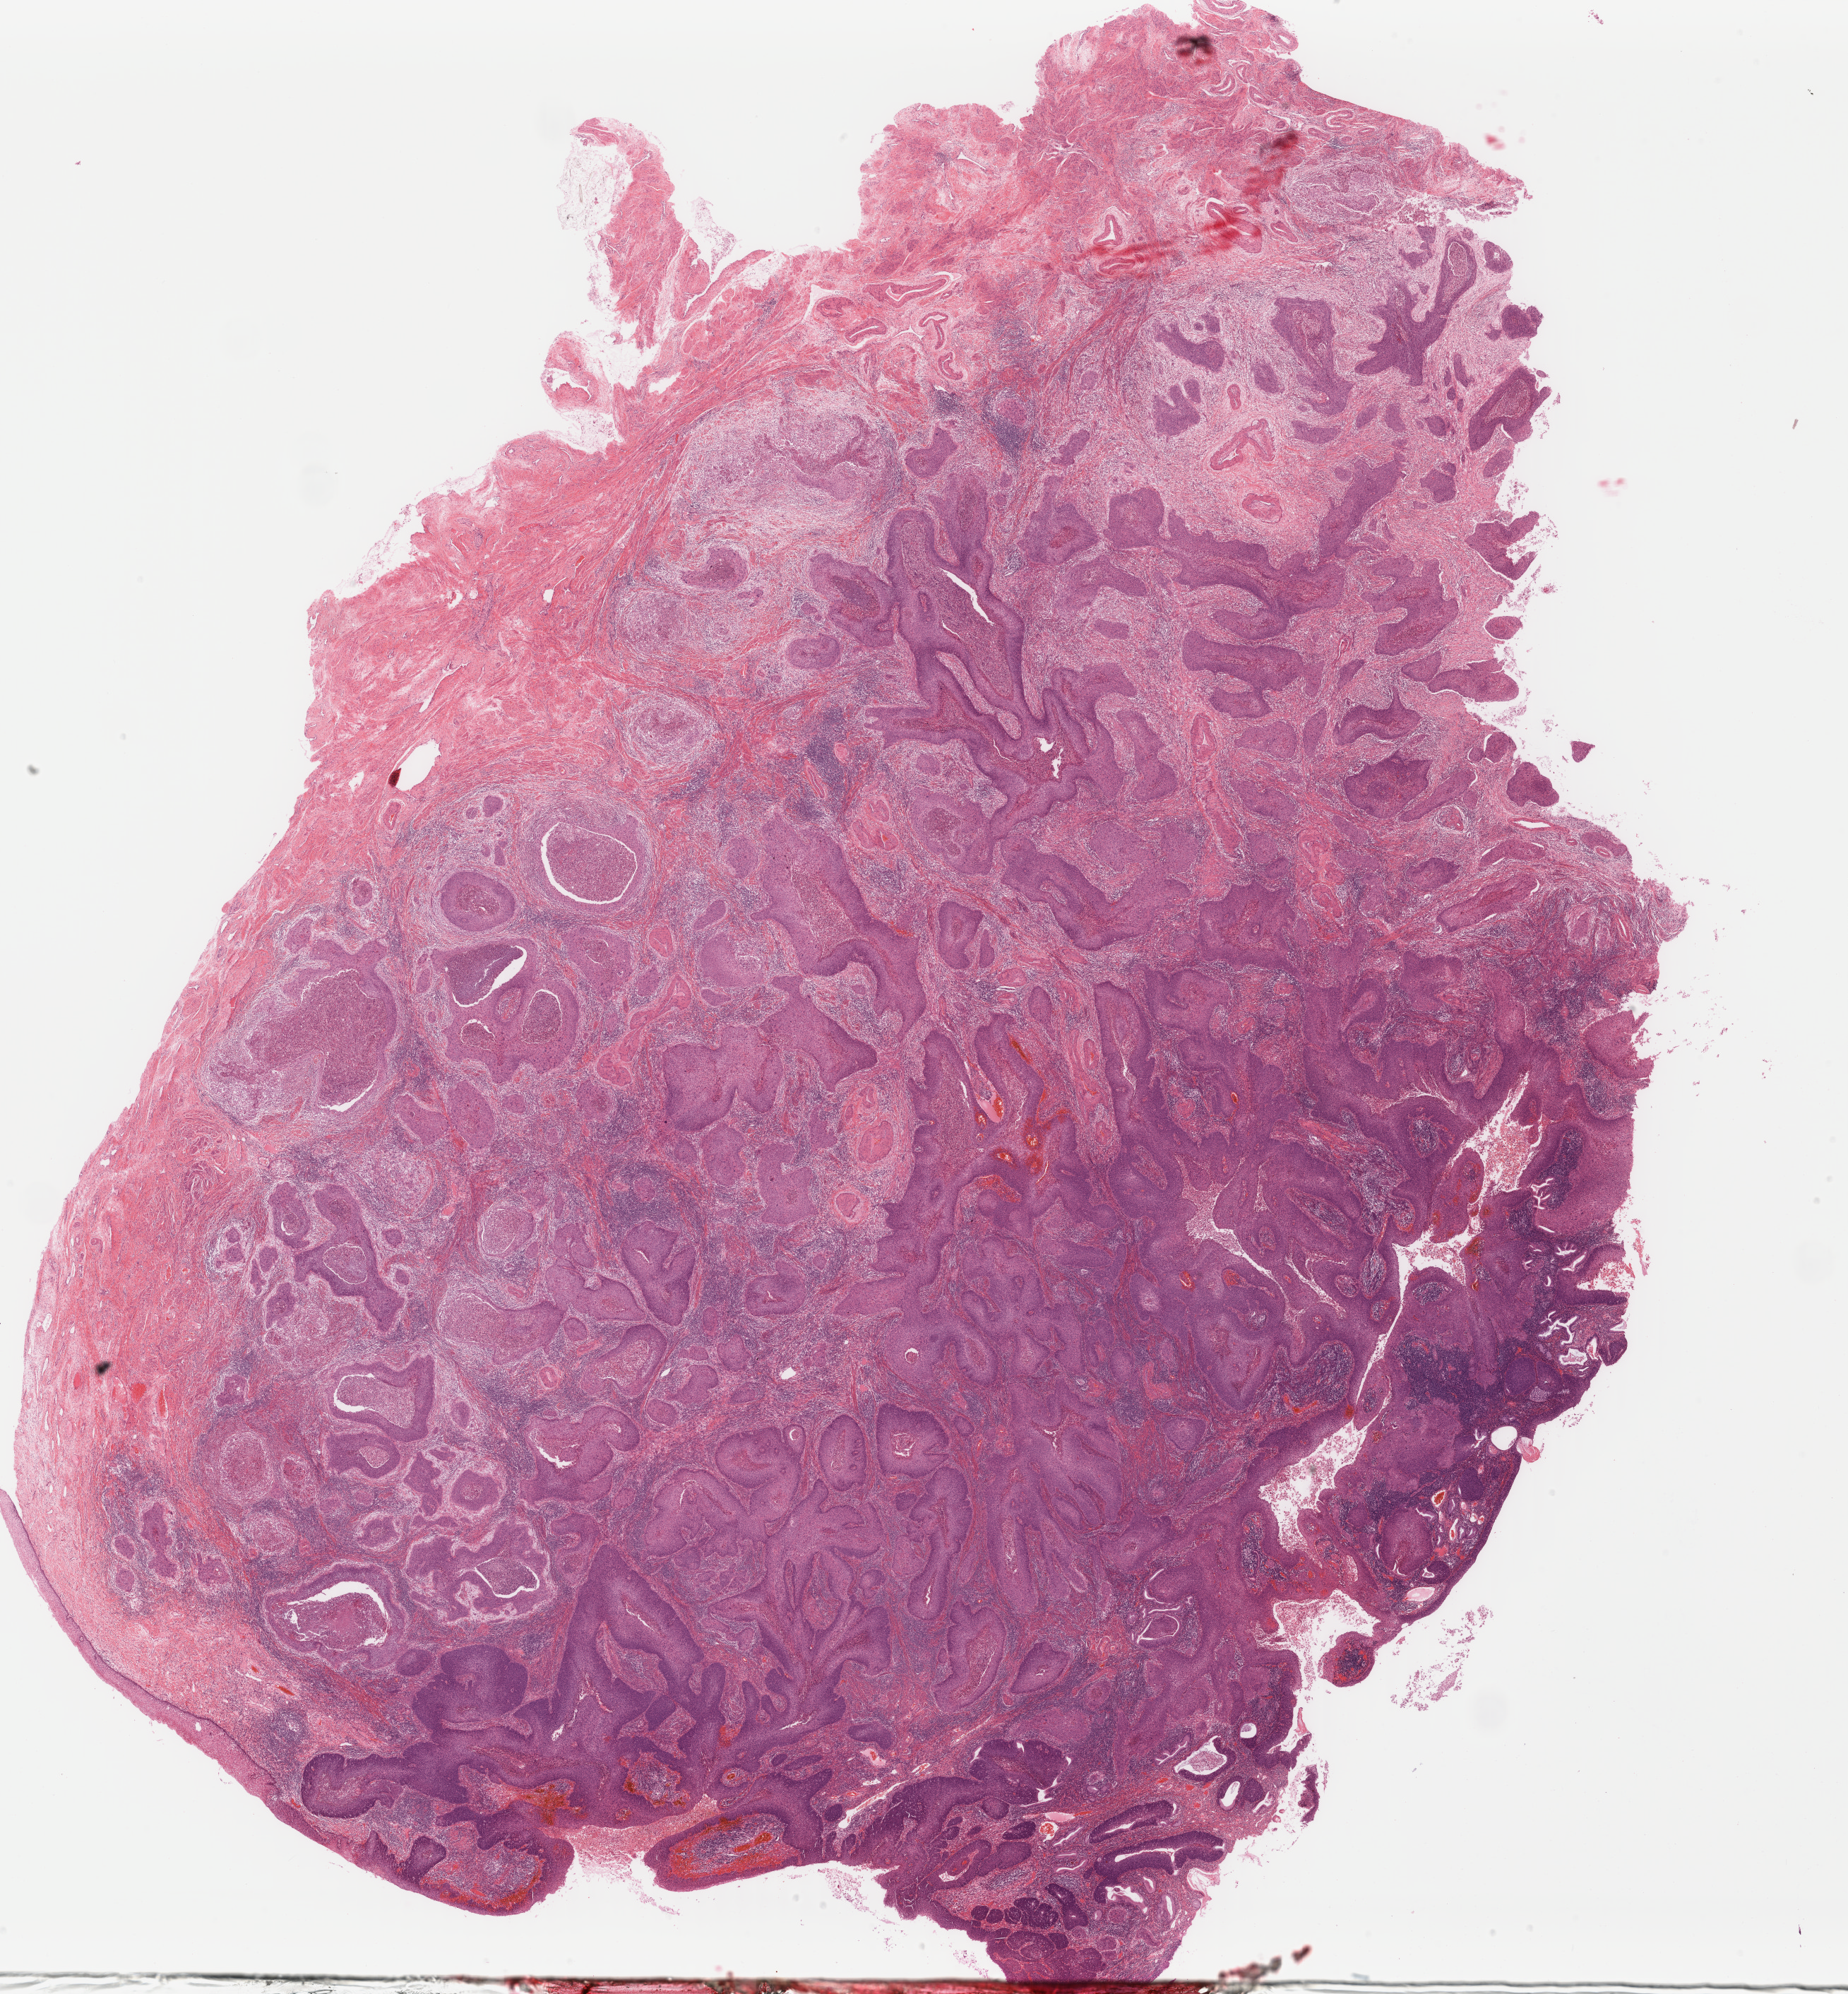
H&E whole-slide image — shown as a low-resolution overview of the whole scanned area (about 20.8 x 22.4 mm, from a 40x scan), FFPE section, primary tumour sample from the cervix. Patient: female, age at initial diagnosis 54 years. Histologic grade: G2 (moderately differentiated).
• FIGO stage: IB1
• diagnosis: Squamous cell carcinoma, NOS (cervix uteri)